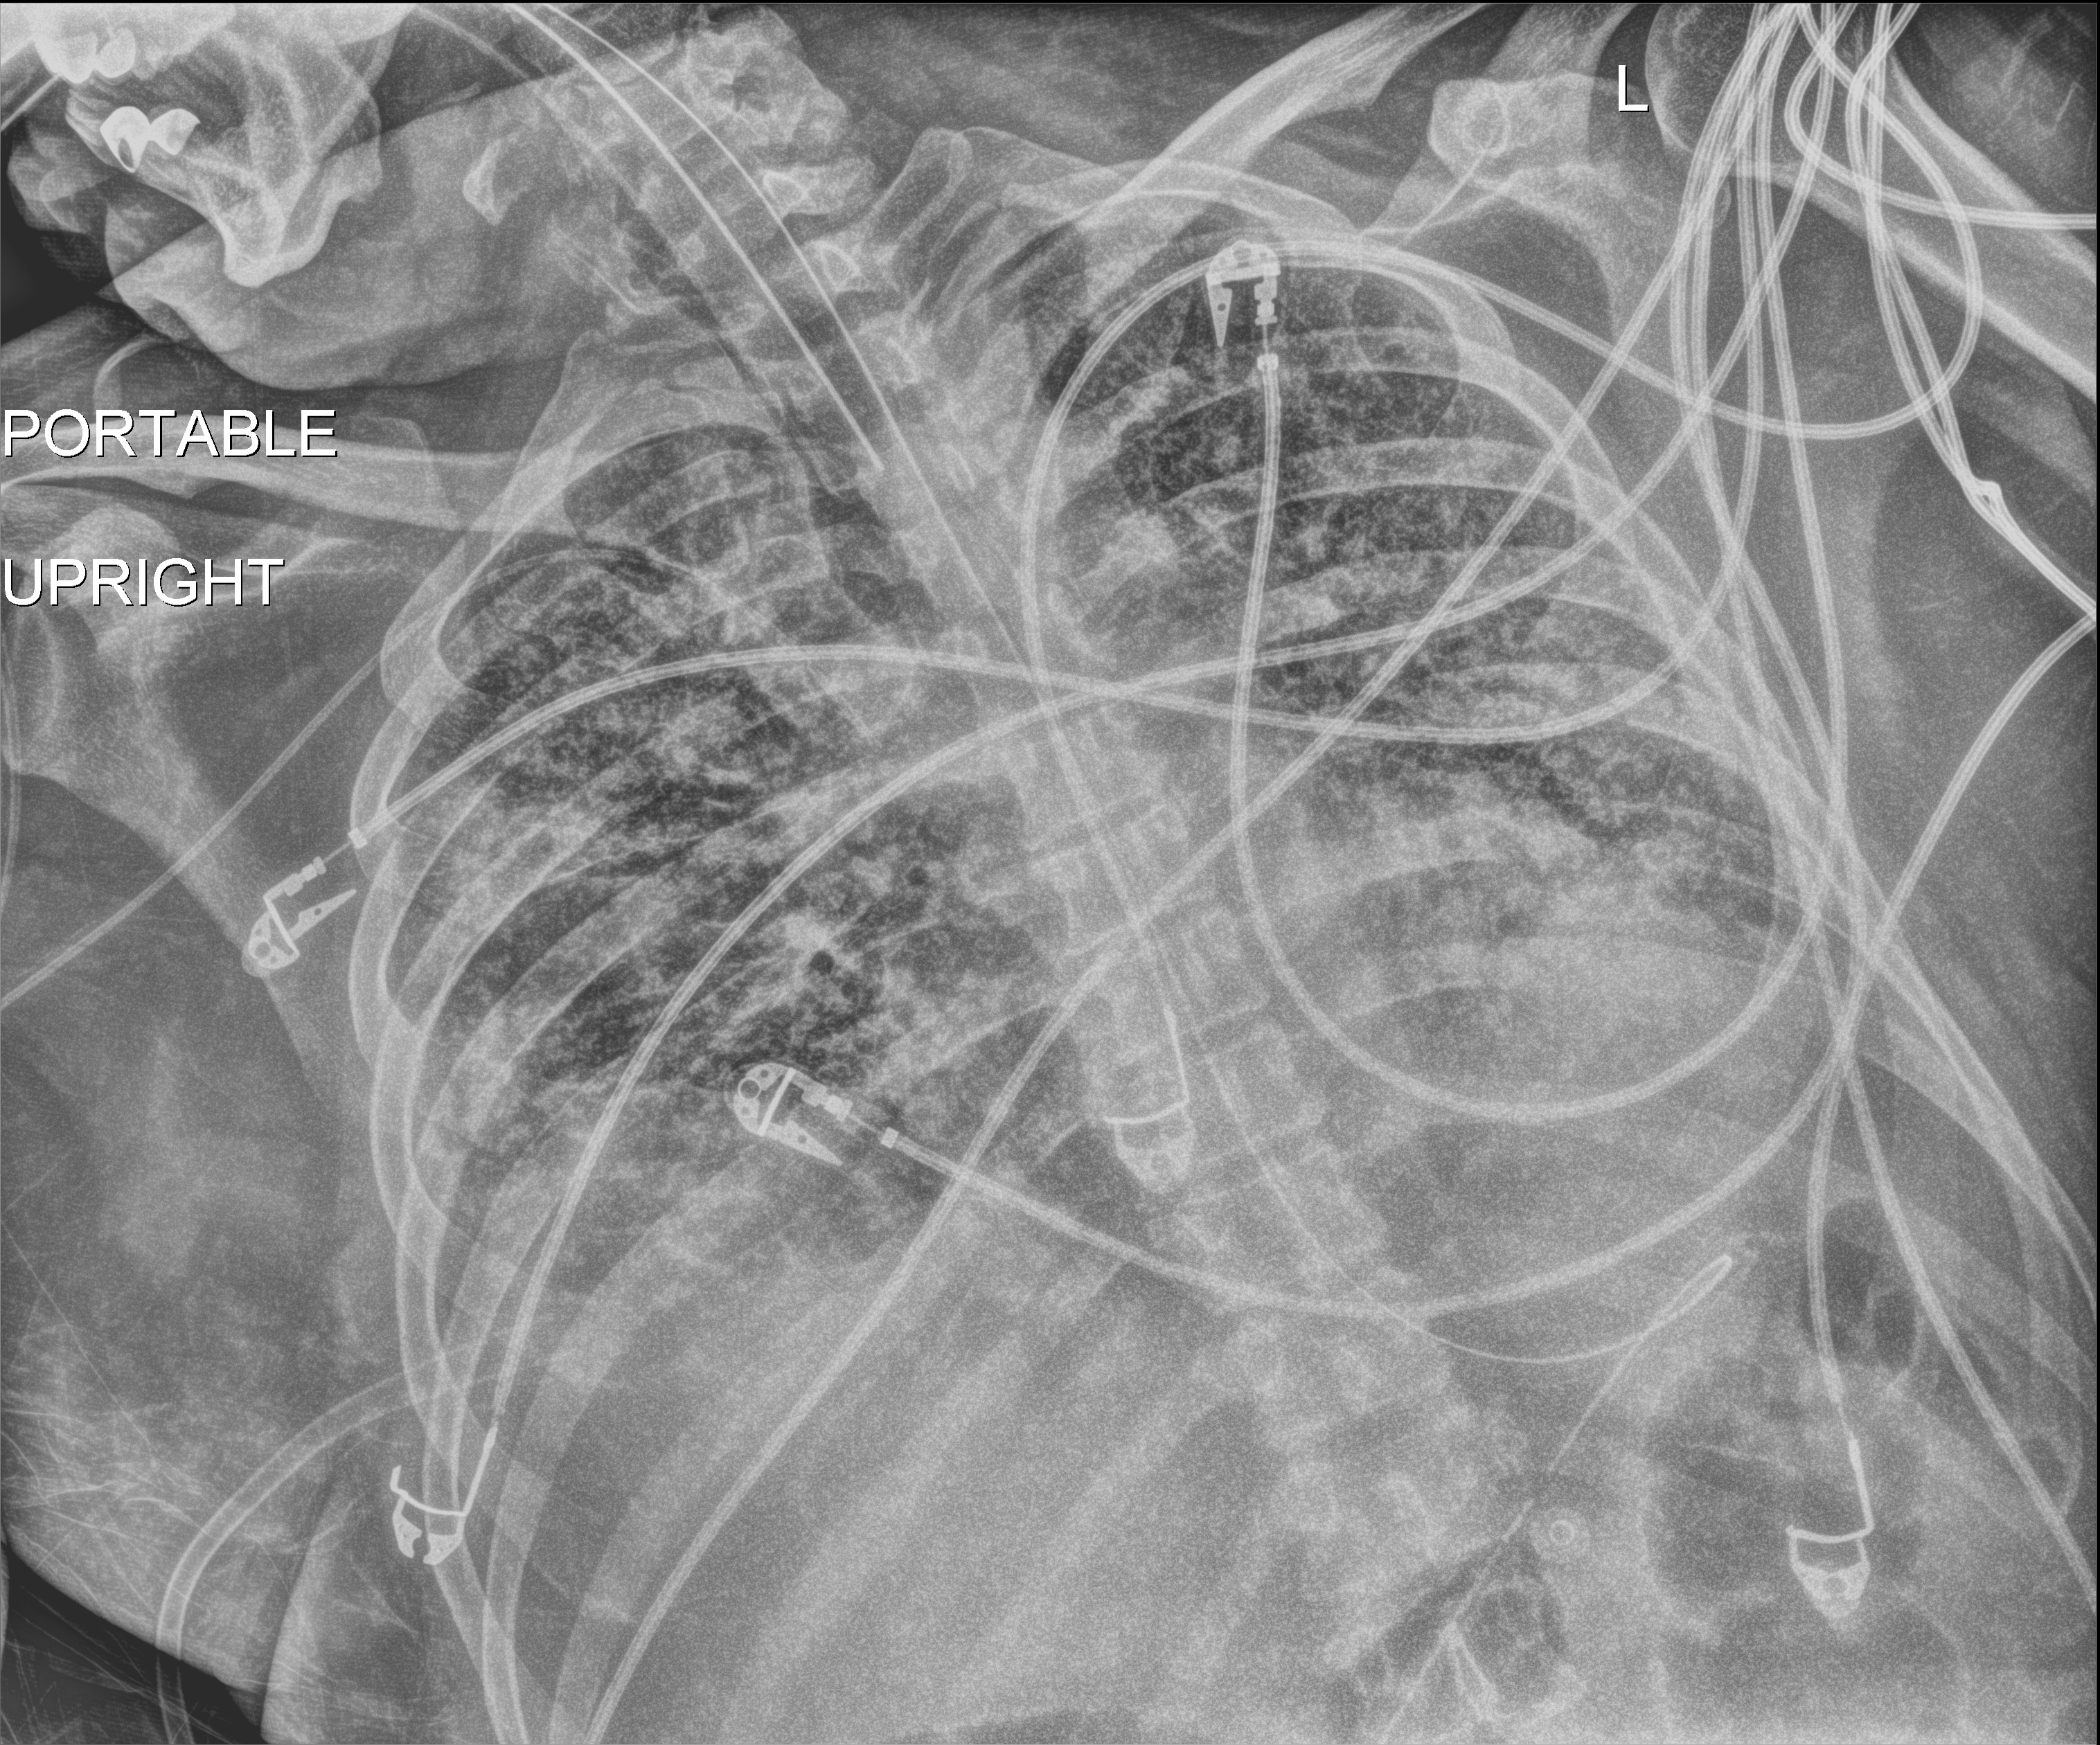
Portable chest radiograph, anteroposterior (AP) projection. Male patient hospitalised with COVID-19, age 18–59 years.
Hospital-stay facts (about this admission, not read from this image; timing relative to this image not recorded): mechanically ventilated during this hospital stay: yes.